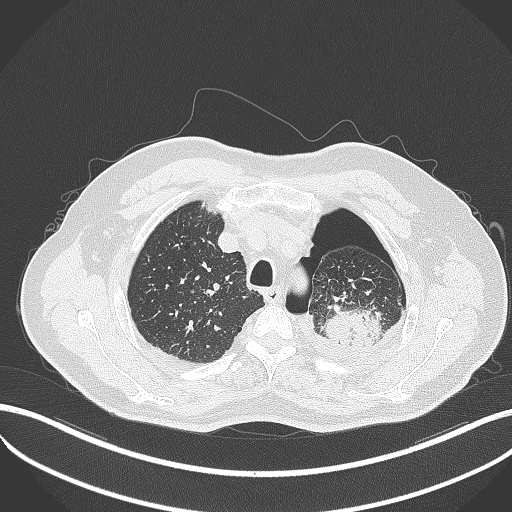
Chest CT, one axial slice. Slice 411 of 464 in the series (ordered by position). 120 kVp. Lung window (W 1500 / L -600 HU). 1 mm slice thickness. 512 × 512 image matrix, field of view 400 × 400 mm. Patient: male, 76 years. From the clinical record (not read from this slice): clinical TNM (as recorded): T3 N0 M1b.
Outlined on this slice (rectangle marked by the reading radiologist):
- lung tumour (recorded histology: adenocarcinoma): bounding box <318,300,381,348> (left, top, right, bottom; pixels)